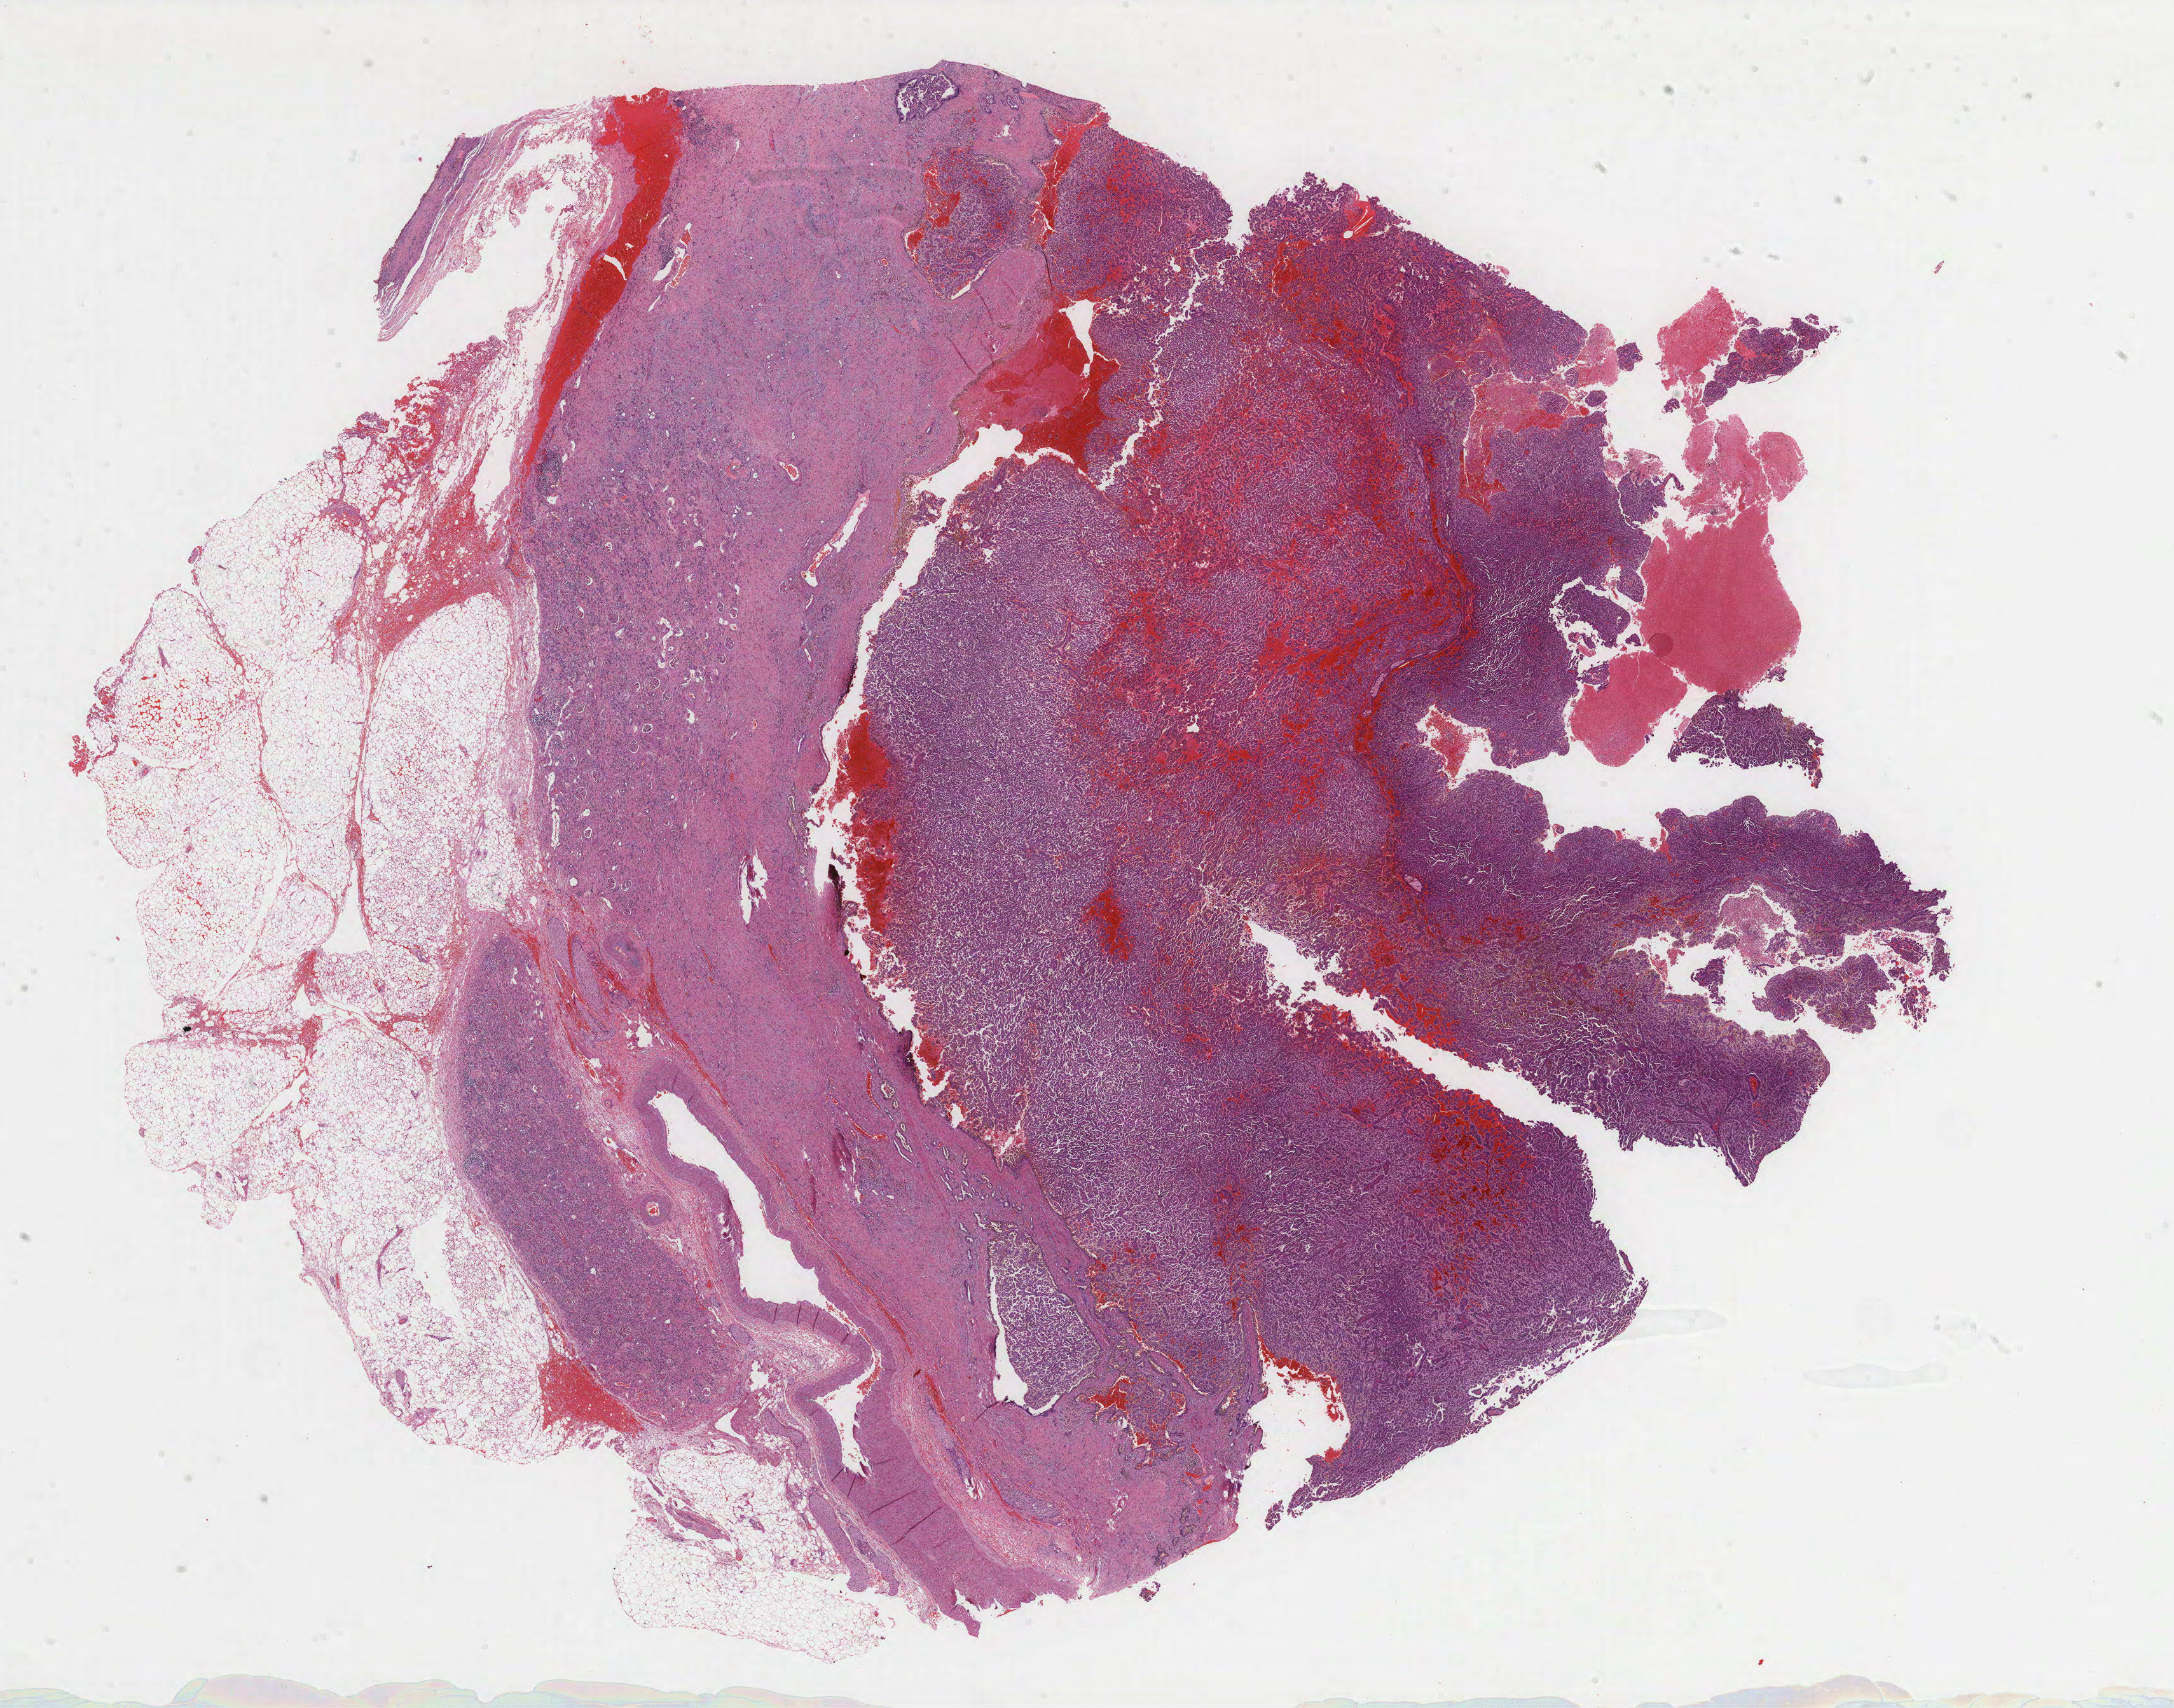
Digitized H&E tissue section (whole slide) — a low-resolution overview of the entire scanned area, about 27.6 x 21.7 mm (acquisition: 40x scan); formalin-fixed paraffin-embedded (FFPE) diagnostic section; sample: primary tumour, kidney. Male, age 59 years at initial diagnosis.
- TNM: T1a NX MX
- pathologic diagnosis: Papillary adenocarcinoma, NOS
- AJCC pathologic stage: I
- laterality: right